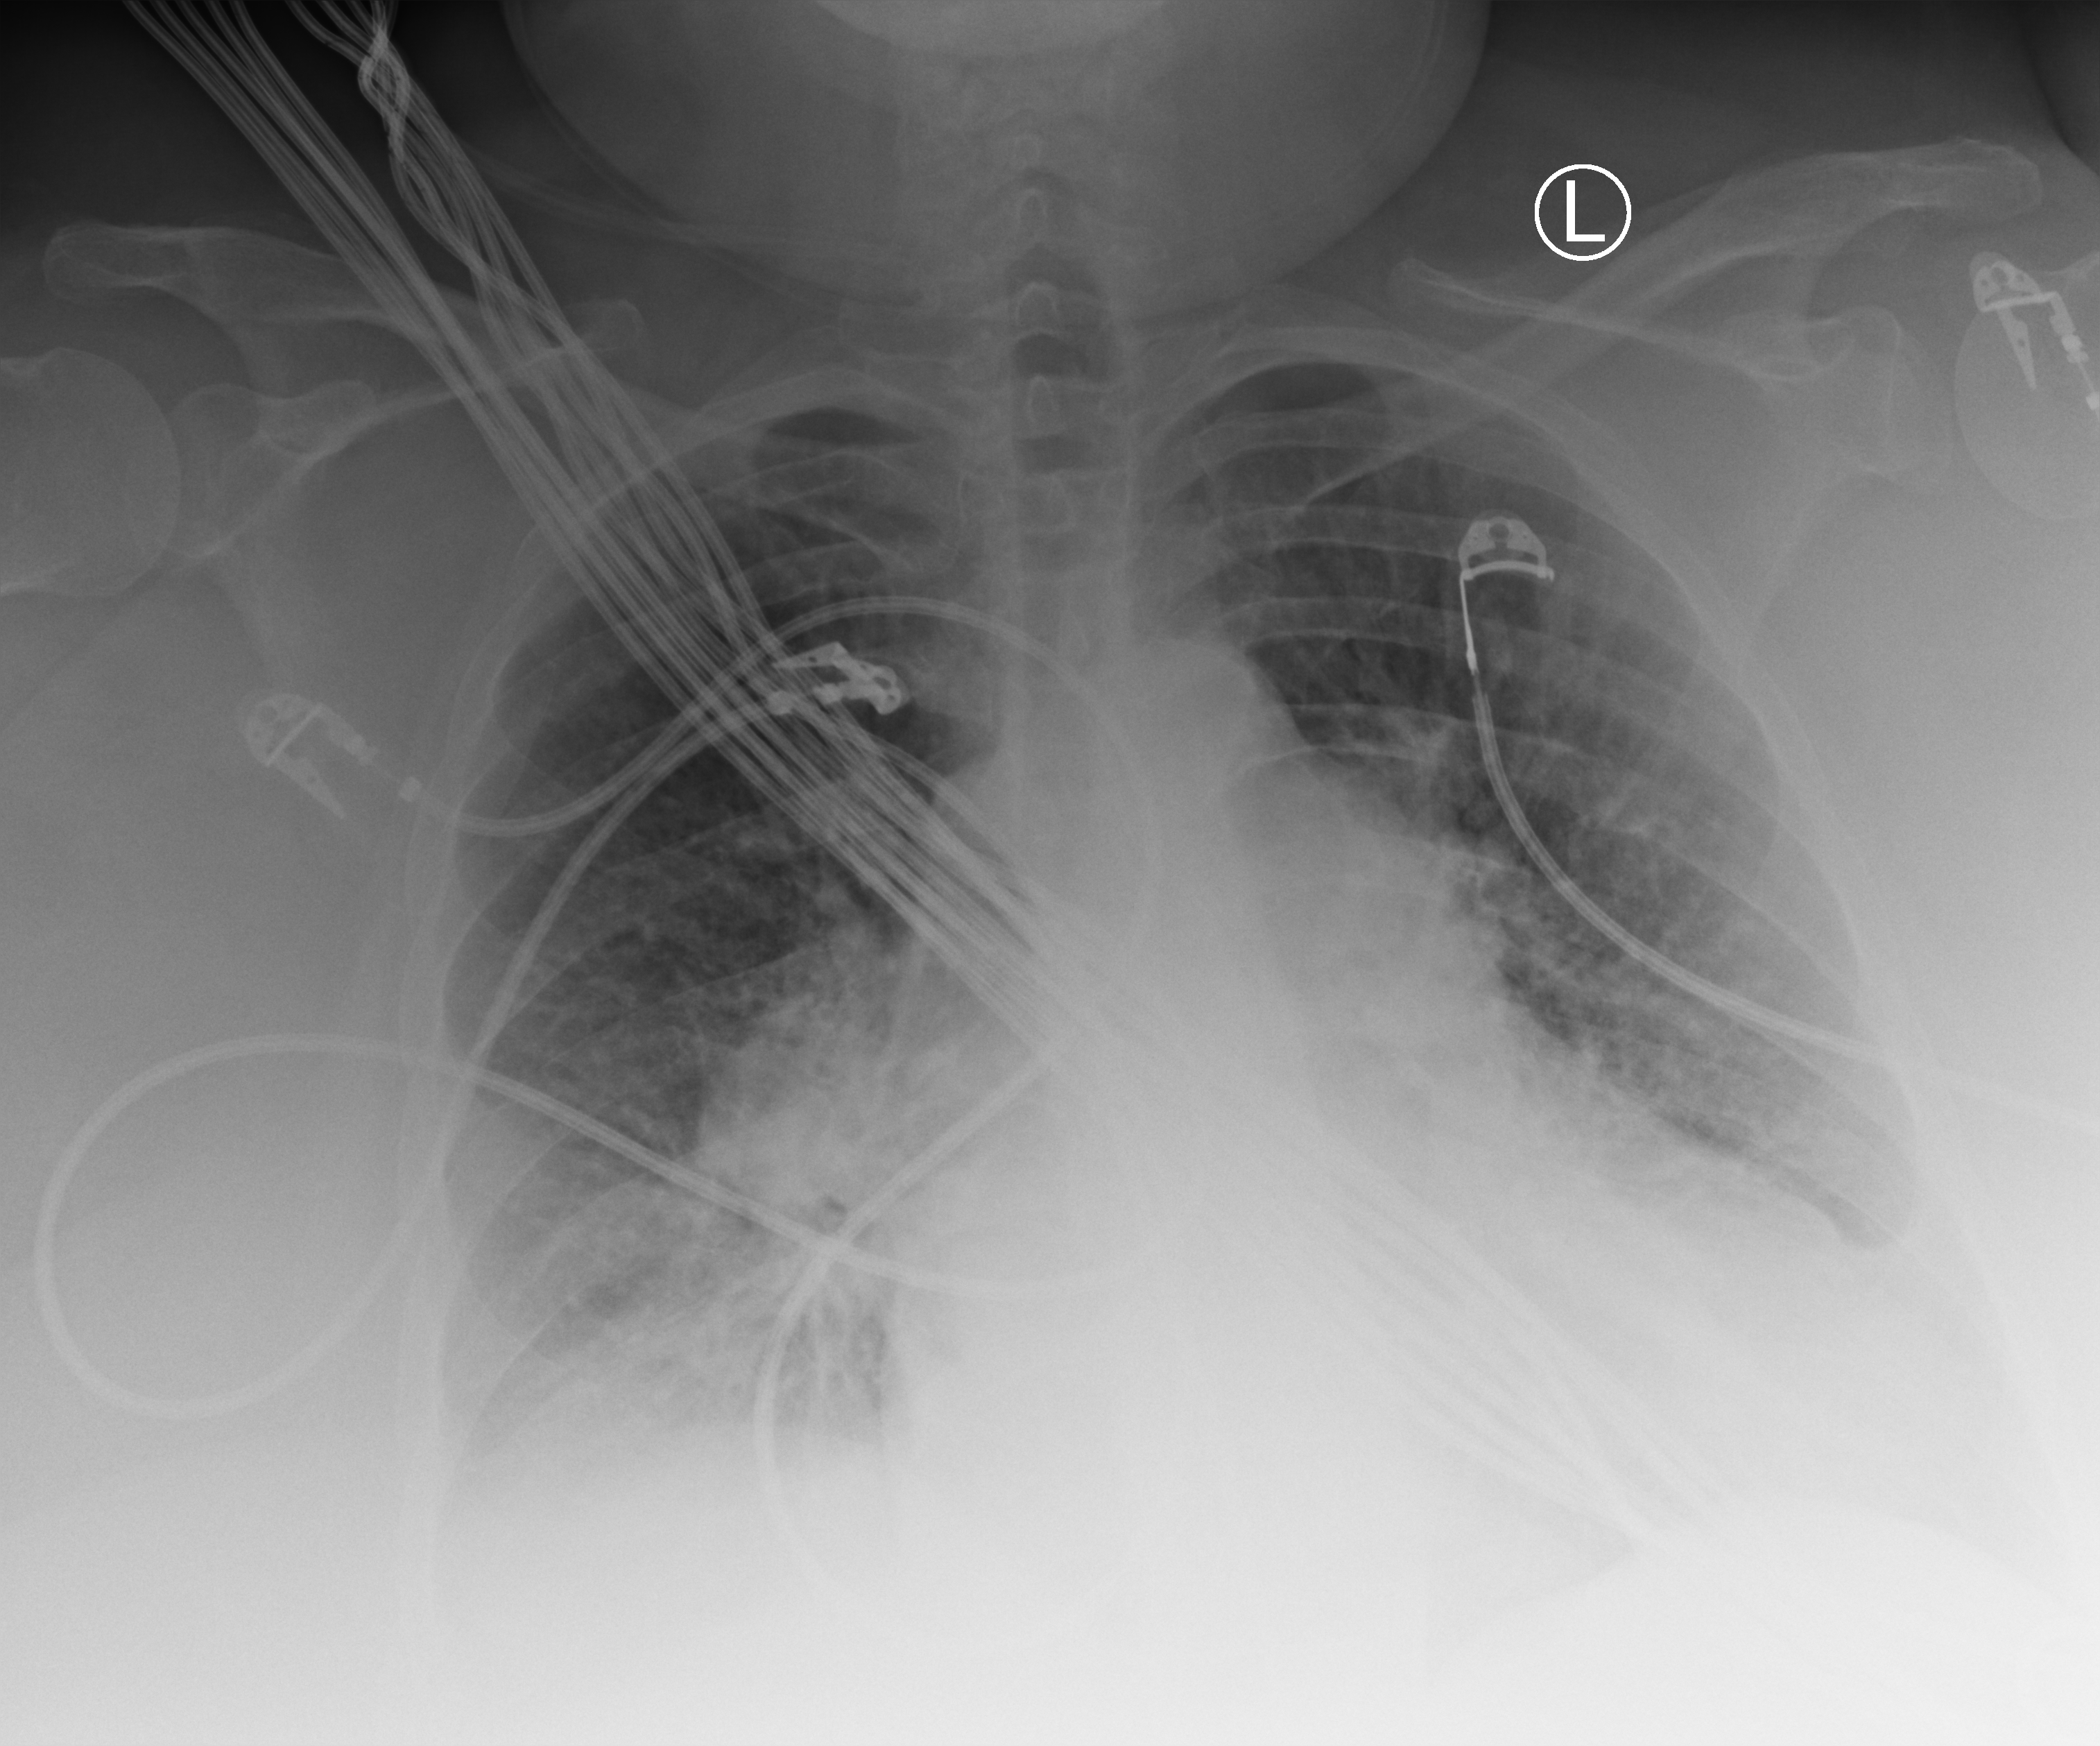
Chest X-ray (portable). Female patient hospitalised with COVID-19, age 60–74 years.
From the hospital-stay record, not from the radiograph (when in the stay this image was taken is not recorded): mechanically ventilated during this hospital stay: yes; hypertension (admission record): yes.